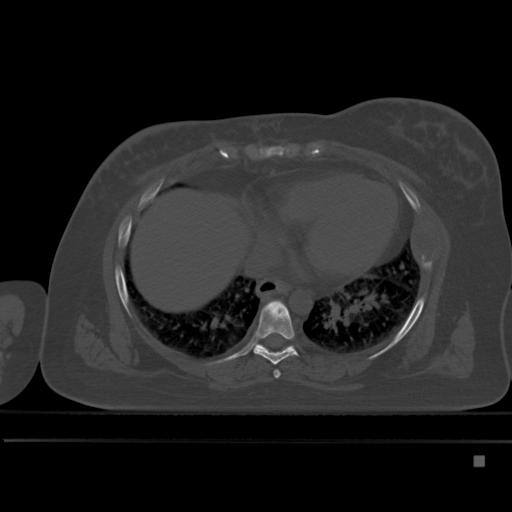
CT including the spine, one axial slice; position 289 of 495 along the scan axis; bone window (W 1800 / L 400 HU); 1.5 mm slice thickness; 512 × 512 image matrix, field of view 404 × 404 mm. Patient: female, 33 years. From the clinical record (not read from this slice): primary cancer: breast; vertebrae with lytic lesions (as recorded): T1.
Annotated regions visible in this slice (semi-automatically segmented with operator editing):
- T6 vertebra: bounding box <274,370,280,378> (left, top, right, bottom; pixels)
- T7 vertebra: <253,300,298,365>
- T8 vertebra: <252,343,295,350>